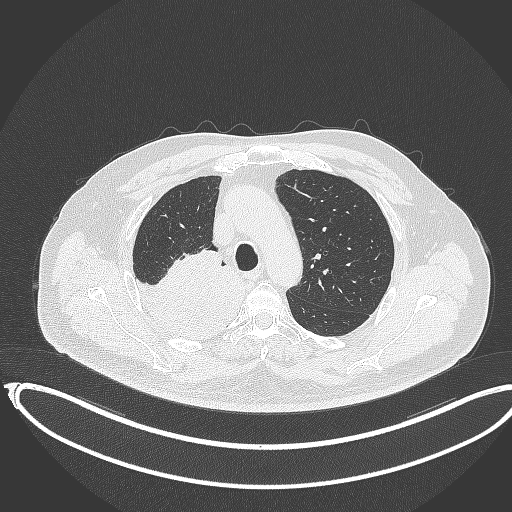
Chest CT, one axial slice. Position 268 of 403 along the scan axis. Reconstruction kernel B70f. 120 kVp. Lung window (W 1500 / L -600 HU). 512 × 512 image matrix, field of view 436 × 436 mm. Male patient, age 68 years. From the clinical record (not read from this slice): clinical TNM (as recorded): T2a N0 M0.
Annotated regions visible in this slice (rectangle marked by the reading radiologist):
- lung tumour (recorded histology: adenocarcinoma): bounding box (x1, y1, x2, y2) in pixels: (126, 246, 248, 345)